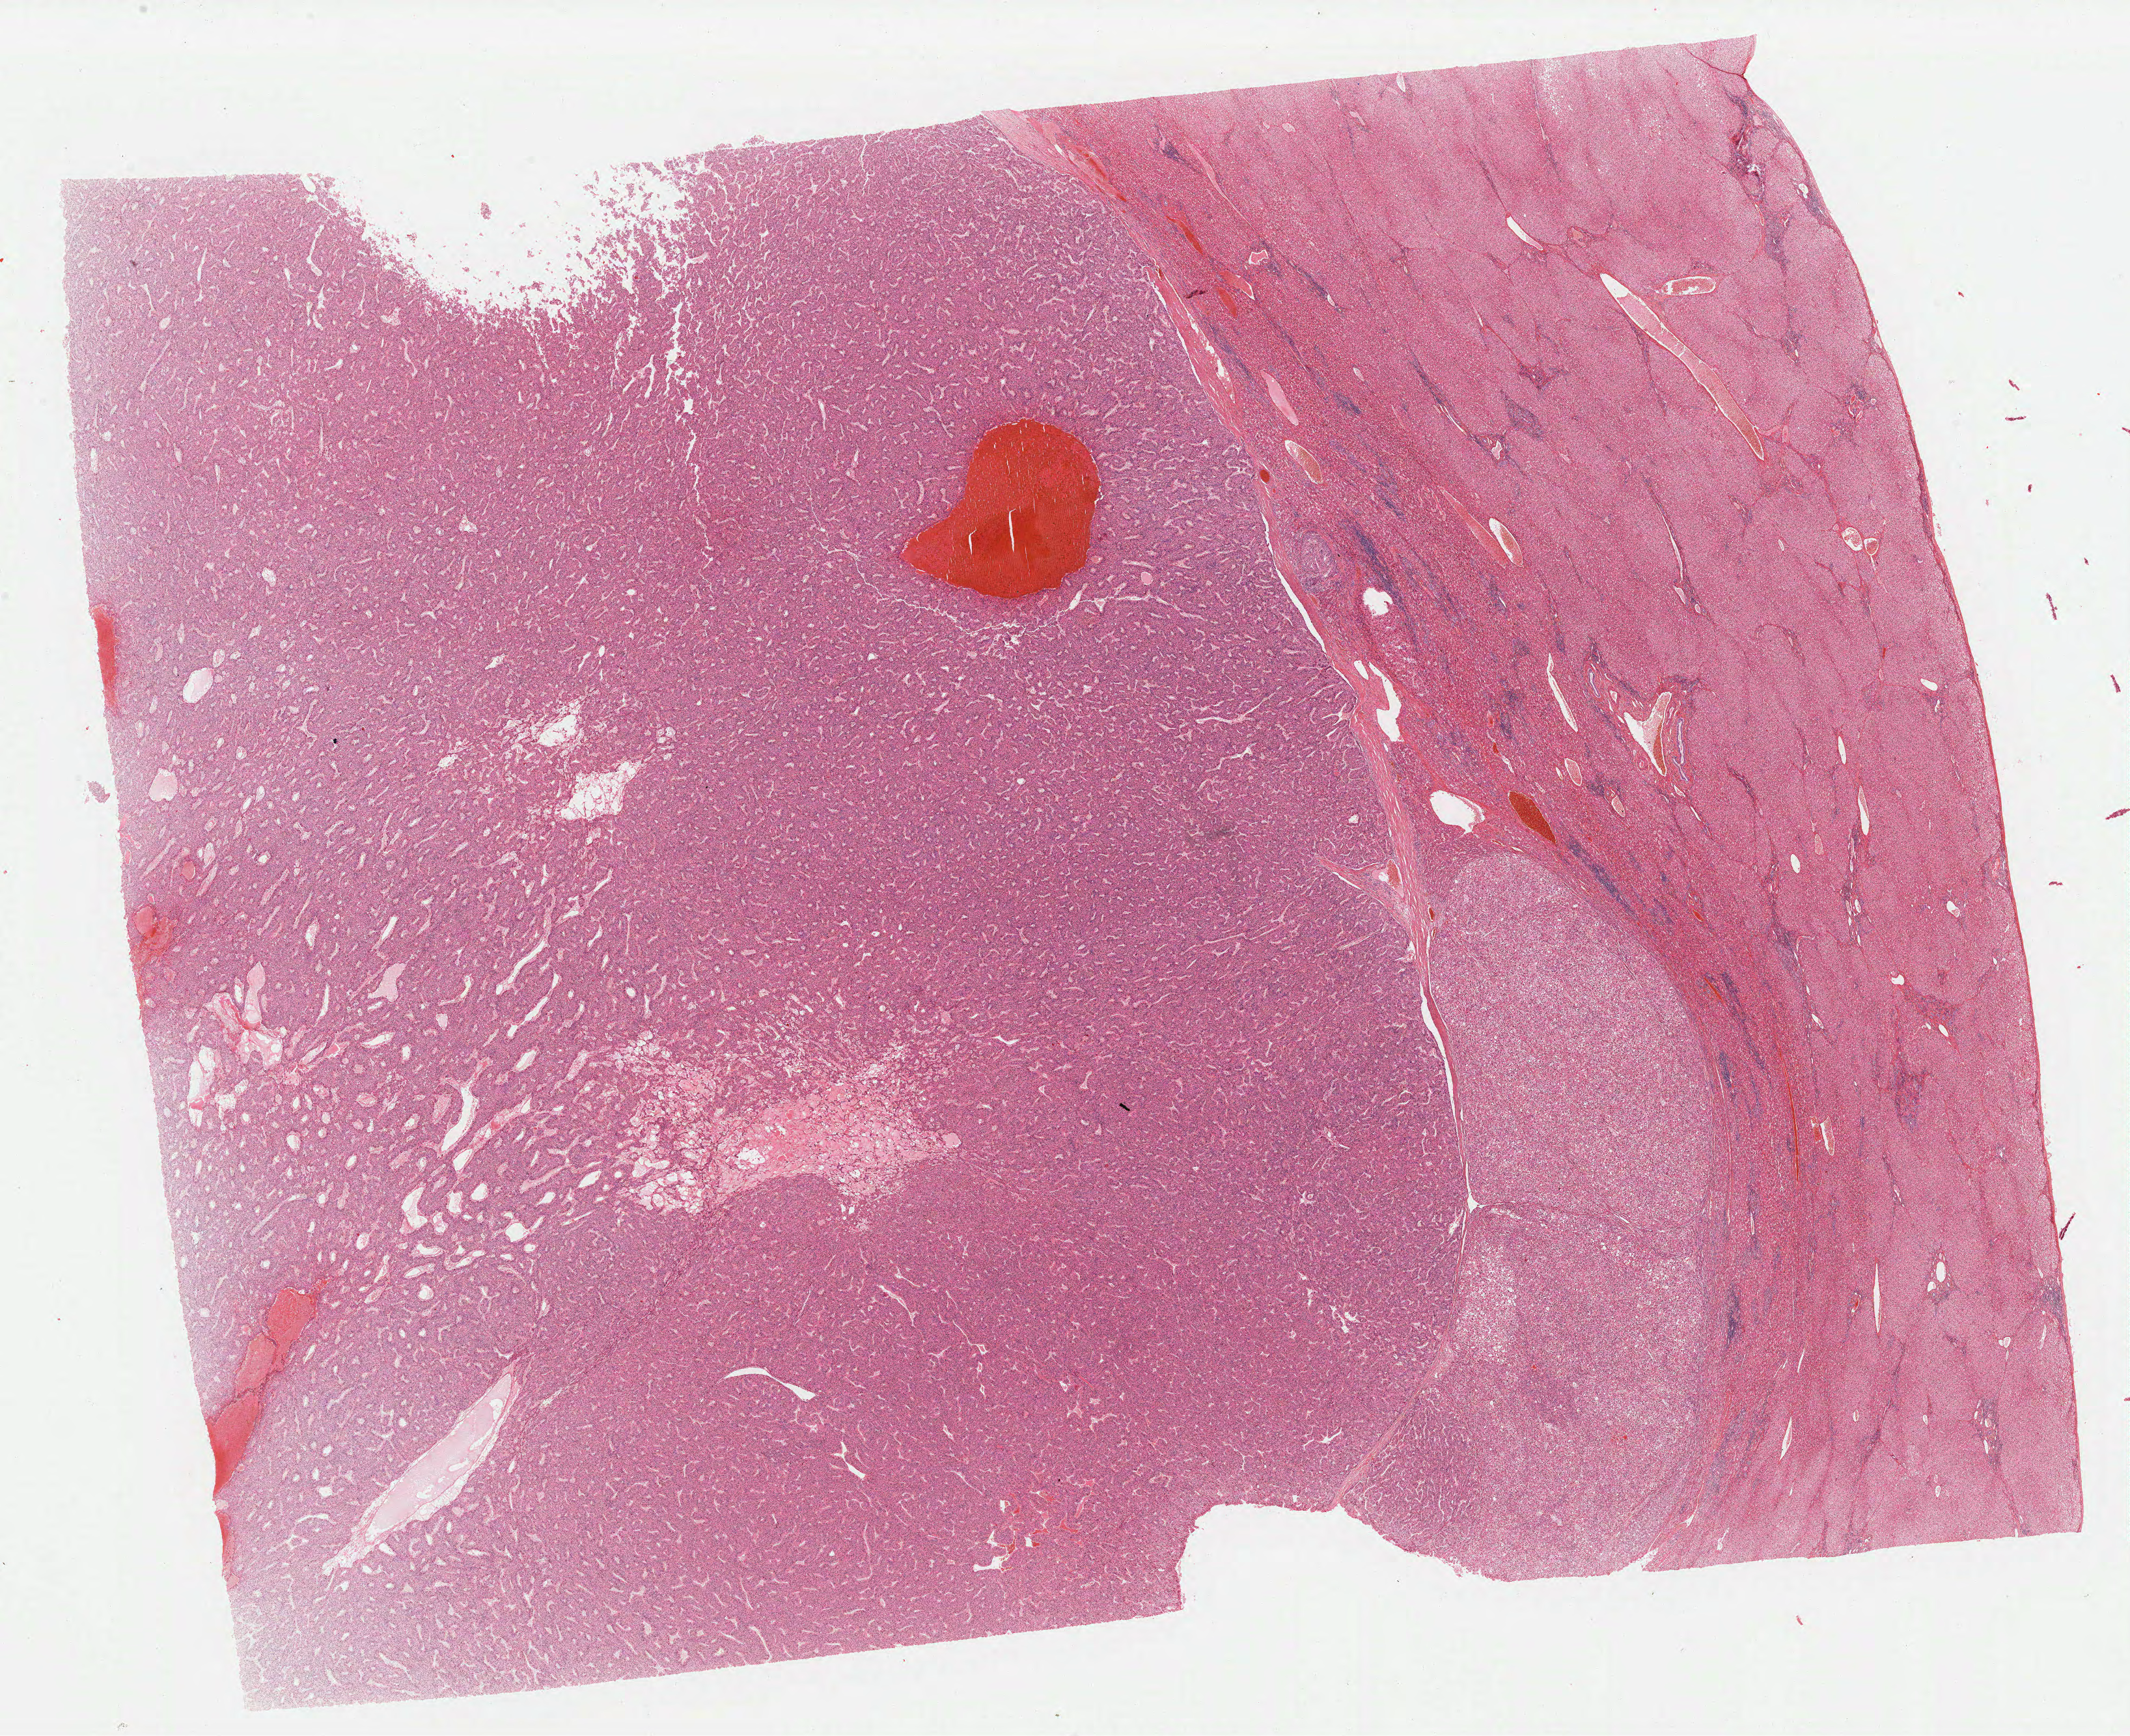
Whole-slide histology image, Hematoxylin and eosin (H&E) stained, a low-resolution overview of the entire scanned area, about 25.9 x 21.1 mm (acquisition: 40x scan), formalin-fixed paraffin-embedded (FFPE) diagnostic section, liver, primary tumour sample. Patient: male, age at initial diagnosis 46 years. Histologic grade: G2 (moderately differentiated).
Histologic diagnosis: Hepatocellular carcinoma, NOS. AJCC pathologic stage: II.